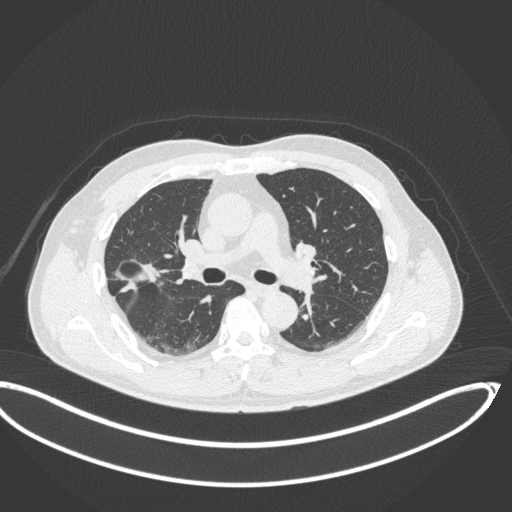
Chest CT, one axial slice. Position 205 of 341 along the scan axis. Reconstruction kernel B31f. 120 kVp. Lung window (W 1500 / L -600 HU). 512 × 512 image matrix, field of view 439 × 439 mm. Male patient, age 63 years. Case-level facts recorded for this patient, not image findings: clinical TNM (as recorded): T1c N0 M0; histopathological grade: G2-3.
Annotated regions visible in this slice (bounding box drawn by a radiologist):
- lung tumour (recorded histology: adenocarcinoma): box from (x=112, y=252) to (x=162, y=297) px